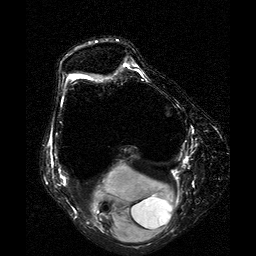
MRI of an extremity soft-tissue mass, one axial slice. Position 11 of 25 along the scan axis. T2-weighted fat-saturated. 256 × 256 image matrix. Female patient. From the clinical record (not read from this slice): histological type: liposarcoma; site of the primary tumour: right thigh.
Outlined on this slice (manually delineated by an expert):
- gross tumour volume (mass): bounding box [x1, y1, x2, y2] px = [89, 162, 179, 246]